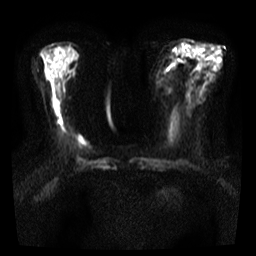
Breast MRI, one axial slice. Position 14 of 35 along the scan axis. Diffusion-weighted series; image 2 of 4 stored at this slice position (different b-values; order by instance number). 3 T. 5 mm slice thickness. 256 × 256 image matrix, field of view 300 × 300 mm. Female patient.
Structures marked on this image (expert manual segmentation):
- tumour on diffusion-weighted imaging: bounding box (x1, y1, x2, y2) in pixels: (72, 133, 86, 152)